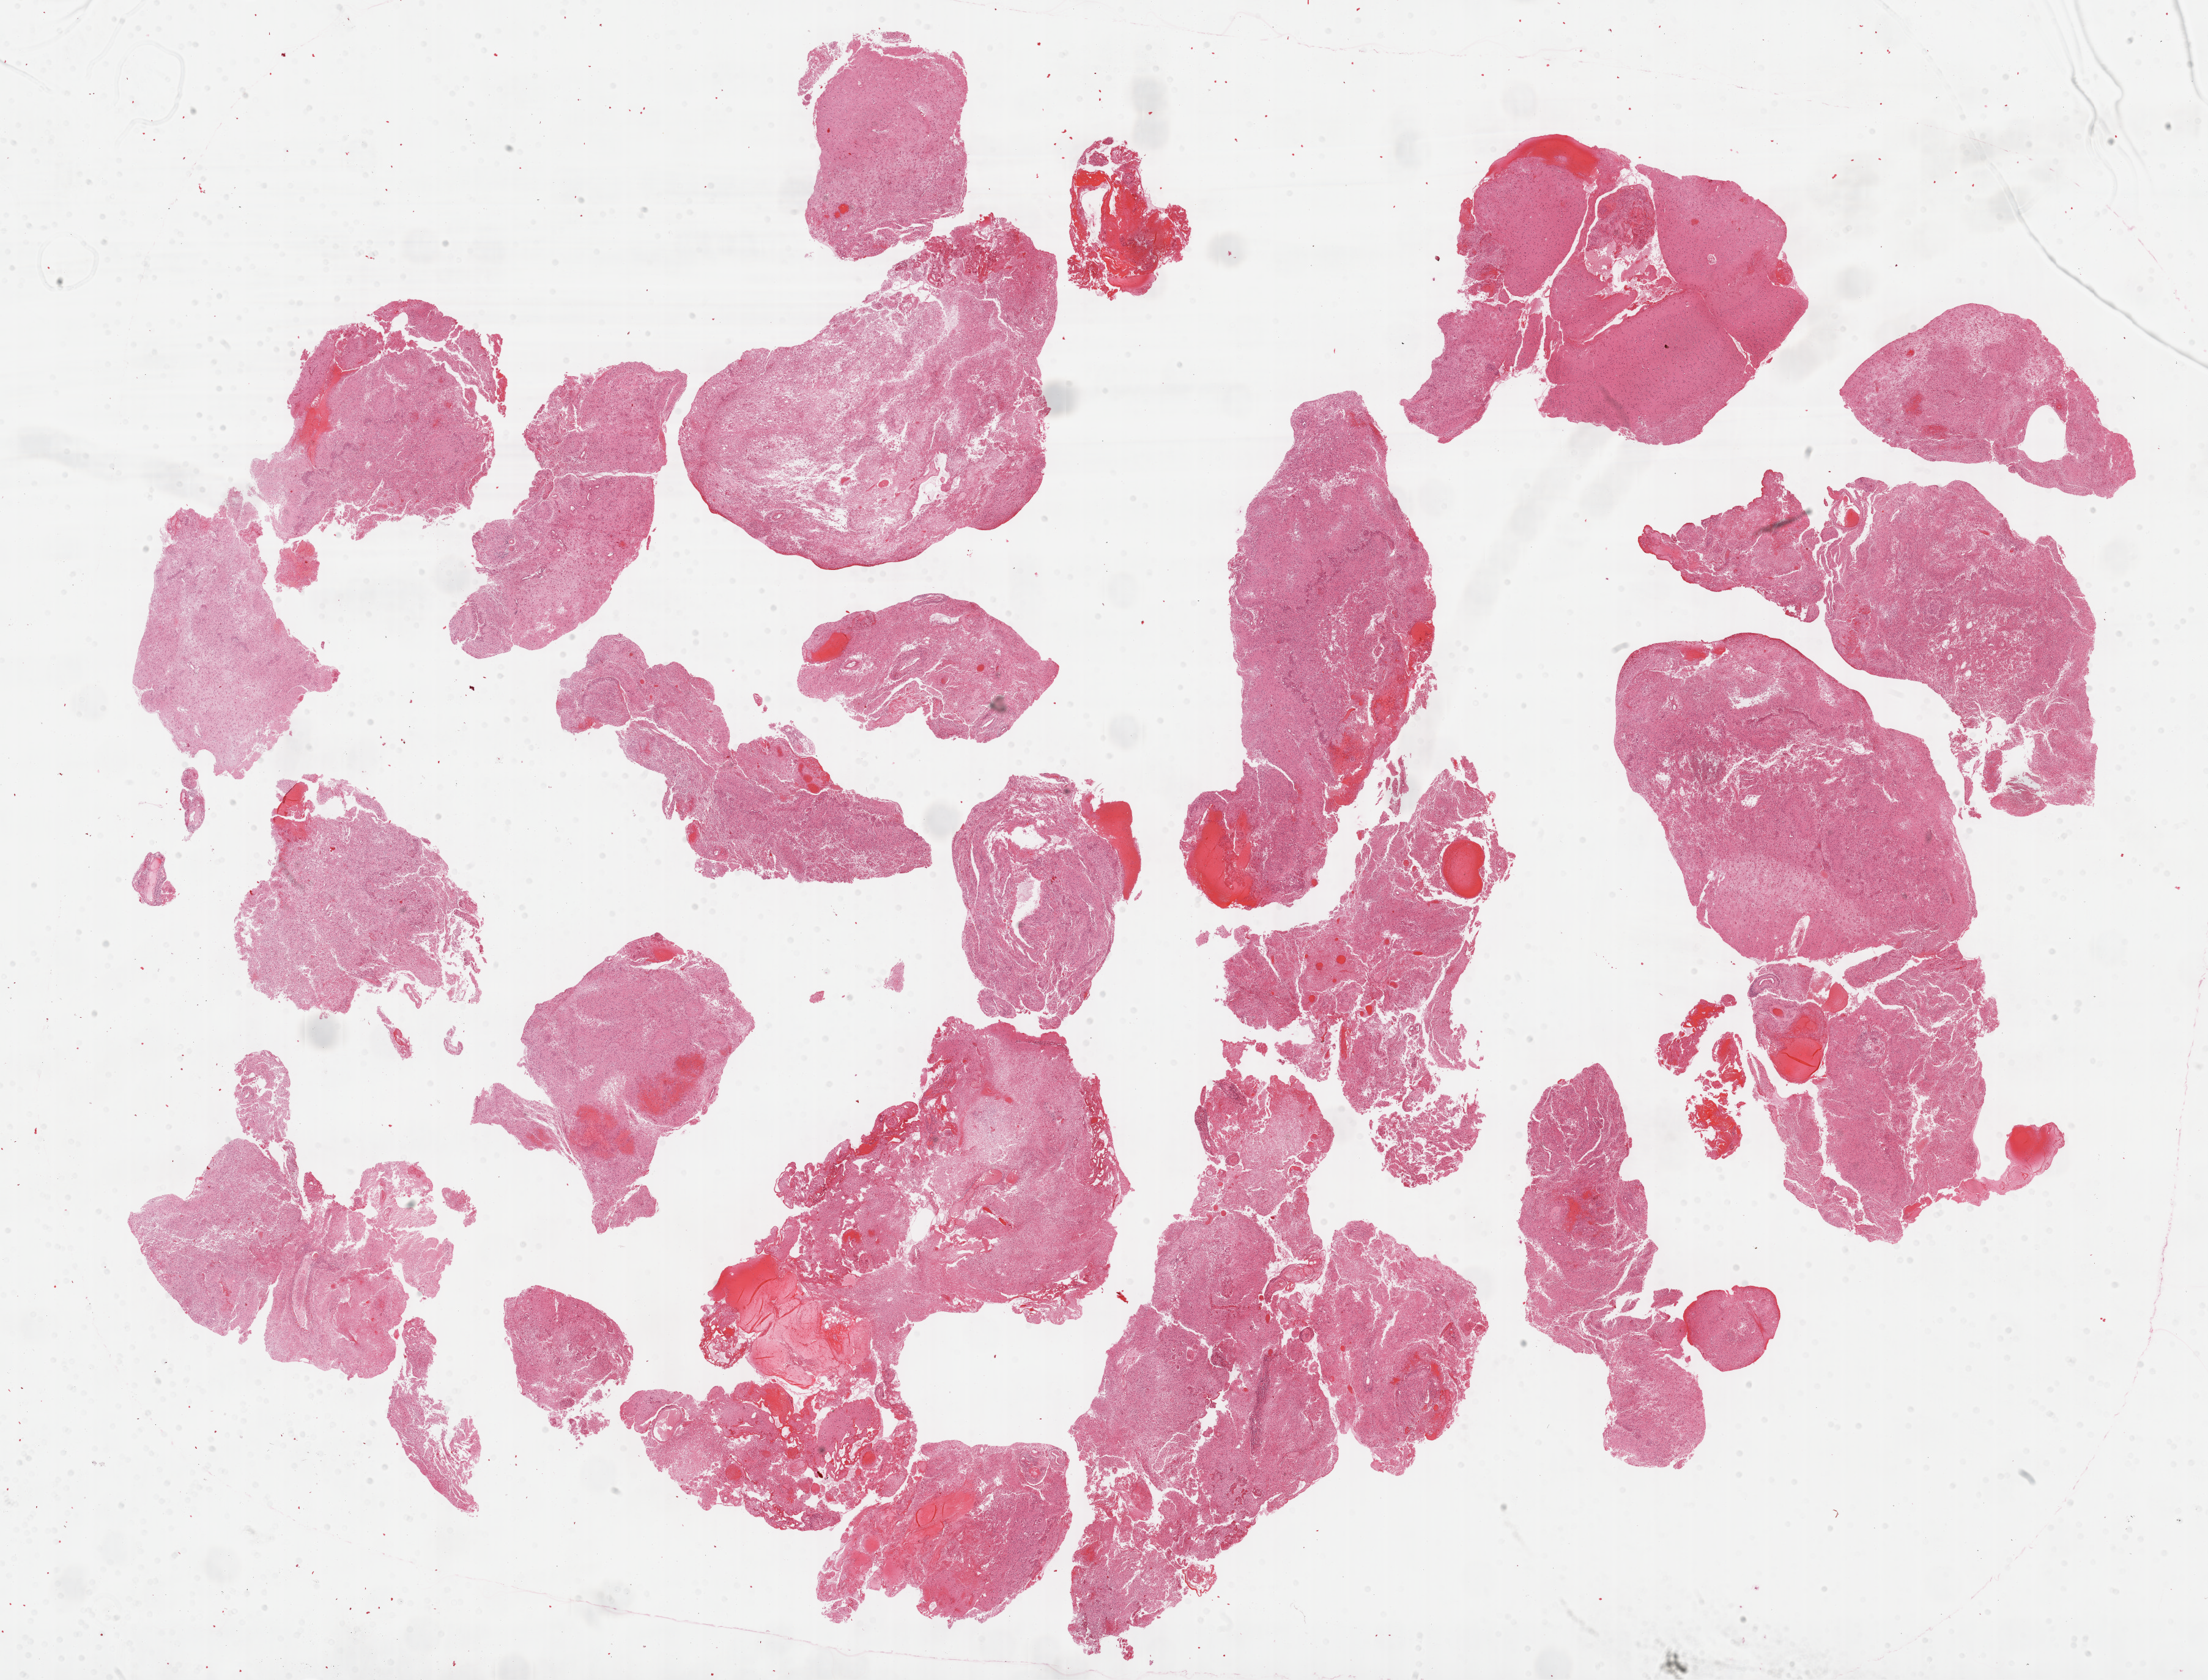
Whole-slide histology image, H&E — whole scanned area (about 29.2 x 22.2 mm) shown as a low-resolution overview; formalin-fixed paraffin-embedded (FFPE) diagnostic section; primary tumour sample from the brain. Male patient; age at initial diagnosis 81 years.
• pathologic diagnosis: Glioblastoma